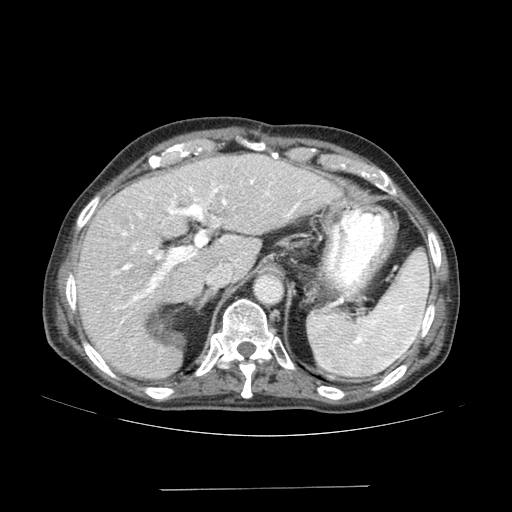
Contrast-enhanced abdominal CT (liver protocol), one axial slice; slice 112 of 192 in the series (ordered by position); reconstruction kernel SOFT; 120 kVp; soft-tissue window (W 400 / L 40 HU); 512 × 512 image matrix. Case-level facts recorded for this patient, not image findings: diagnosis: hepatocellular carcinoma (patient treated with transarterial chemoembolisation; whether this scan precedes or follows treatment is not stated here); TNM stage (as recorded): Stage-IVA; Child-Pugh class: A; tumour differentiation: poorly differentiated; tumour nodularity: uninodular.
Annotated regions visible in this slice (semi-automatic segmentation, software-assisted and operator-edited):
- liver parenchyma outside the tumour (the mass and vessels are separate outlines, so this box may not span the whole liver): bounding box (x1, y1, x2, y2) in pixels: (76, 154, 342, 378)
- liver vessels: (113, 179, 300, 324)